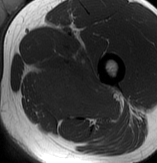
MRI of an extremity soft-tissue mass, one axial slice. Slice 56 of 70 in the series (ordered by position). MR volume resampled by the dataset authors to the PET/CT grid (not the native acquisition matrix). 3.27 mm slice thickness. 157 × 163 image matrix. Male patient. Case-level facts recorded for this patient, not image findings: histological type: extraskeletal osteosarcoma; grade: high; site of the primary tumour: left adductur.
Annotated regions visible in this slice (expert contour drawn on MRI and transferred to this co-registered scan by the dataset authors):
- gross tumour volume (mass): box from (x=31, y=47) to (x=121, y=123) px